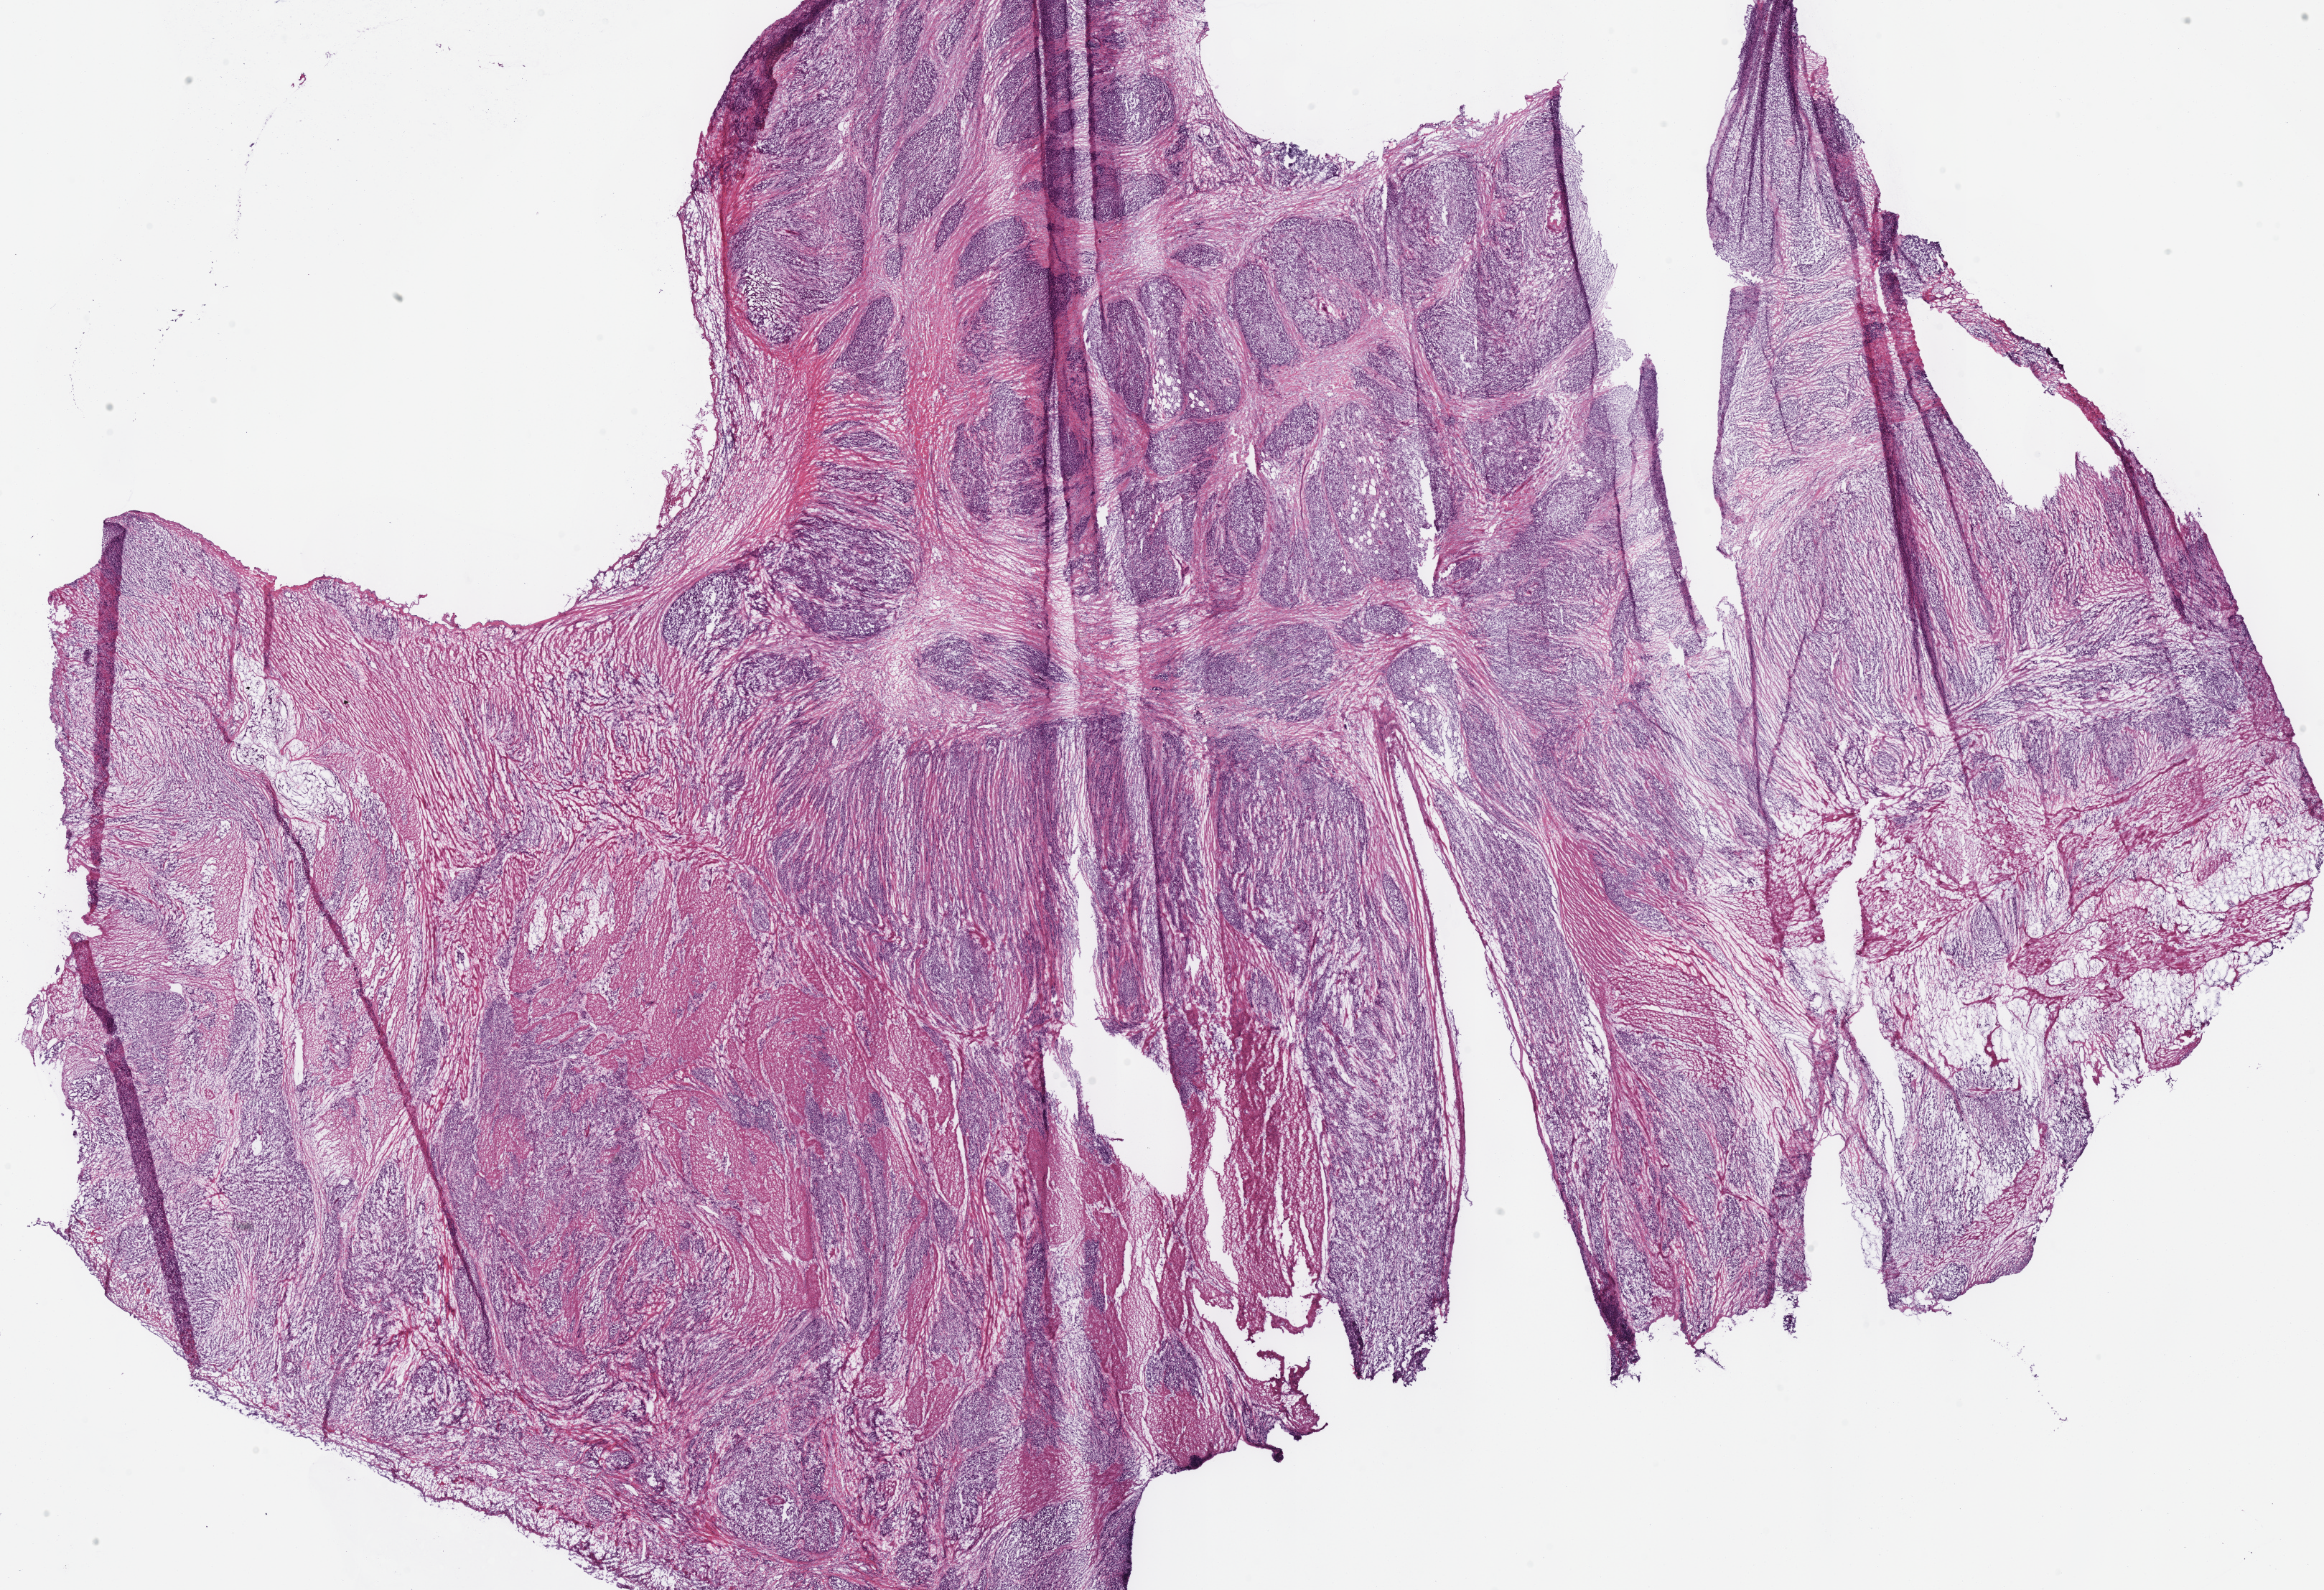
Whole-slide histology image, H&E, shown as a low-resolution overview of the whole scanned area (about 25.5 x 17.4 mm, from a 40x scan); frozen section from the bottom of the tissue portion; sample: primary tumour, stomach. Male patient; age at initial diagnosis 65 years. Histologic grade: G3 (poorly differentiated). Slide review estimates, as recorded: tumour cells 80%, tumour nuclei 70%, normal cells 0%, stromal cells 20%, necrosis 0%.
AJCC pathologic stage: IIIC (7th edition). Pathologic diagnosis: Adenocarcinoma, NOS (fundus of stomach).